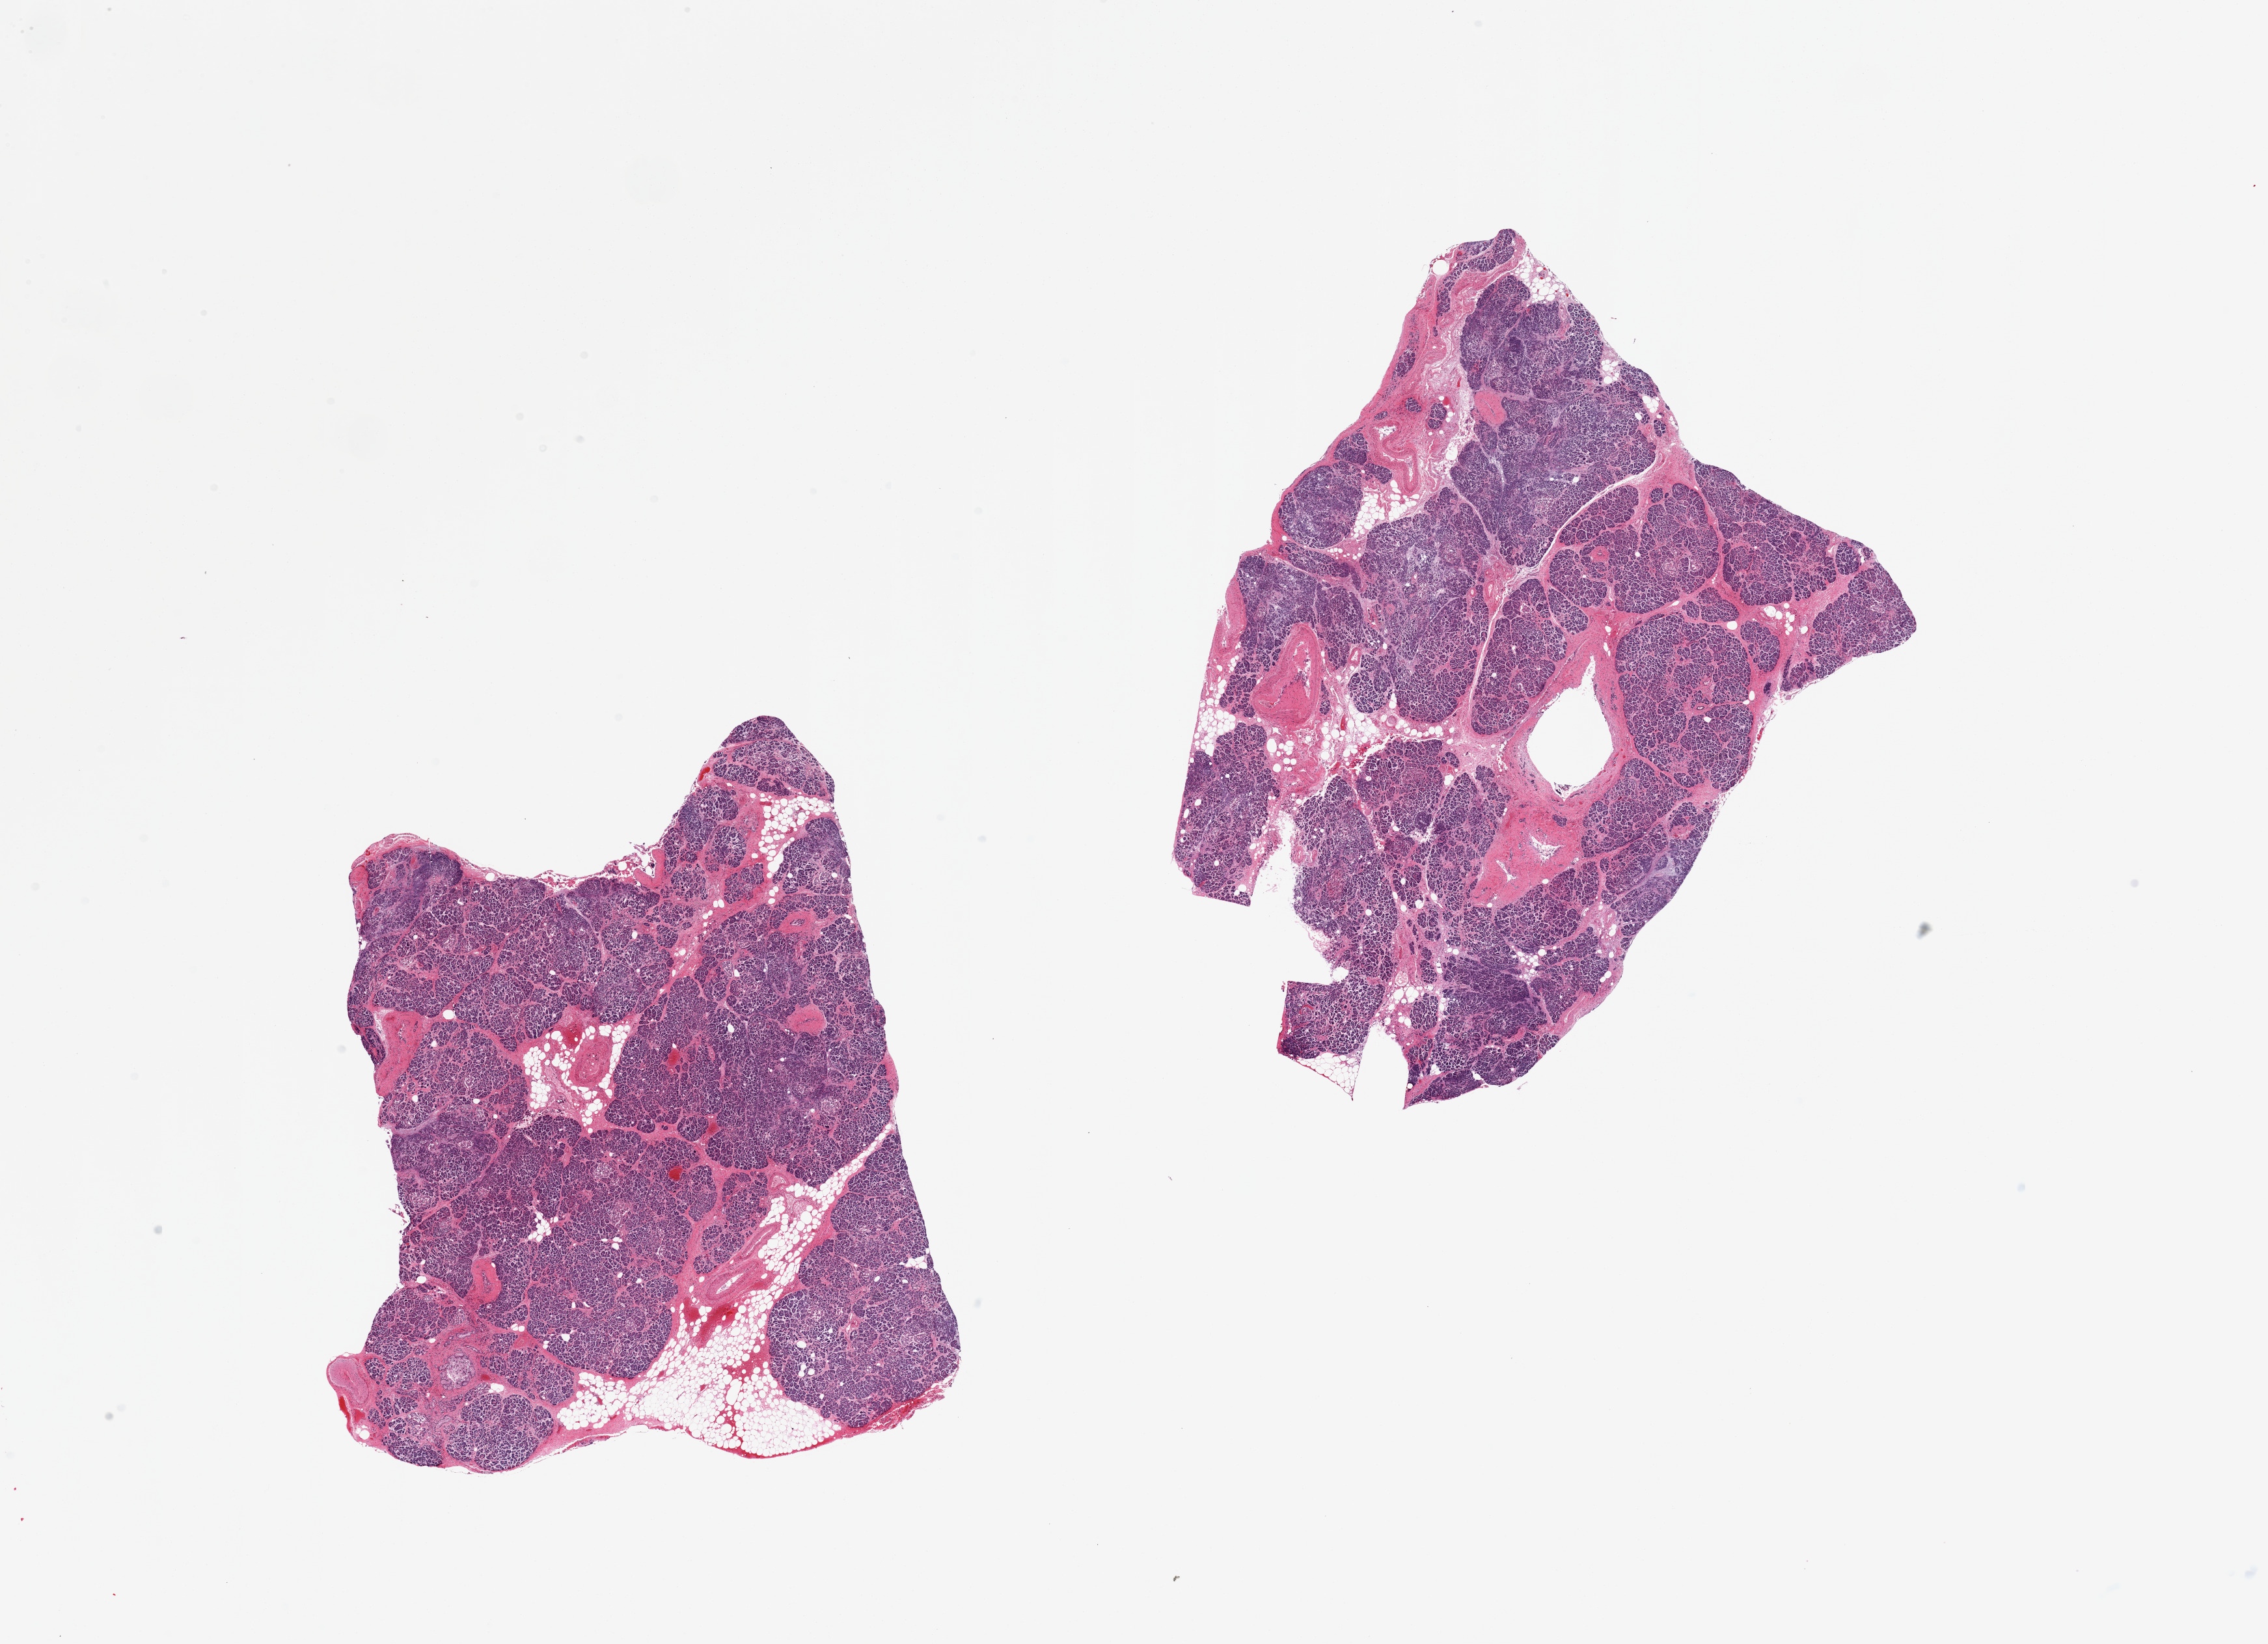
Digitized haematoxylin and eosin-stained section, shown as a low-resolution overview of the whole scanned area (about 27.6 x 20.0 mm), PAXgene-fixed, paraffin-embedded tissue, target tissue: pancreas, tissue donor sample. Female donor.
Review note (as recorded): 2 pieces; islets not diminished; 10% internal fat.